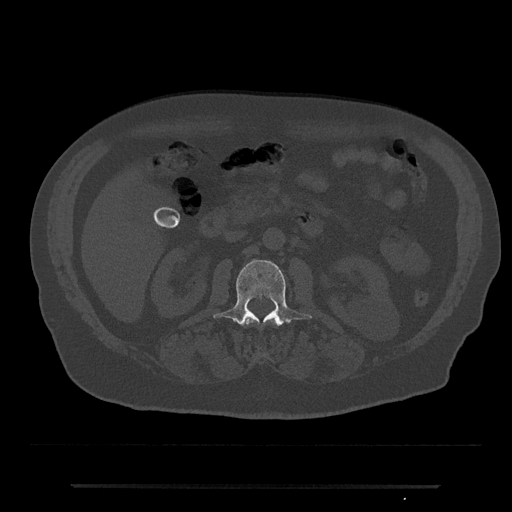
CT including the spine, one axial slice; bone window (W 1800 / L 400 HU); 0.5 mm slice thickness; 512 × 512 image matrix, field of view 434 × 434 mm. Patient: male, 80 years. Case-level facts recorded for this patient, not image findings: primary cancer: prostate; vertebrae with lytic lesions (as recorded): L1, T11.
Annotated regions visible in this slice (semi-automatically segmented with operator editing):
- L1 vertebra: box from (x=243, y=319) to (x=278, y=326) px
- L2 vertebra: (x=213, y=259)–(x=312, y=327)